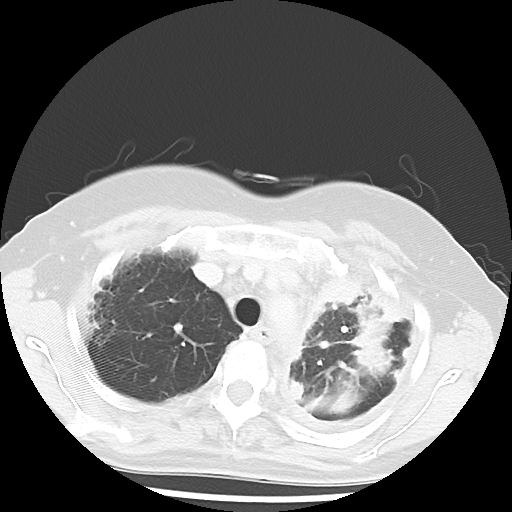
Chest CT, one axial slice. Slice 44 of 56 in the series (ordered by position). Reconstruction kernel LUNG. 120 kVp. Lung window (W 1500 / L -600 HU). 5 mm slice thickness. 512 × 512 image matrix, field of view 309 × 309 mm. Female patient, age 56 years. From the clinical record (not read from this slice): clinical TNM (as recorded): T1c N0 M1.
Structures marked on this image (bounding box drawn by a radiologist):
- lung tumour (recorded histology: adenocarcinoma): bounding box <312,266,369,324> (left, top, right, bottom; pixels)